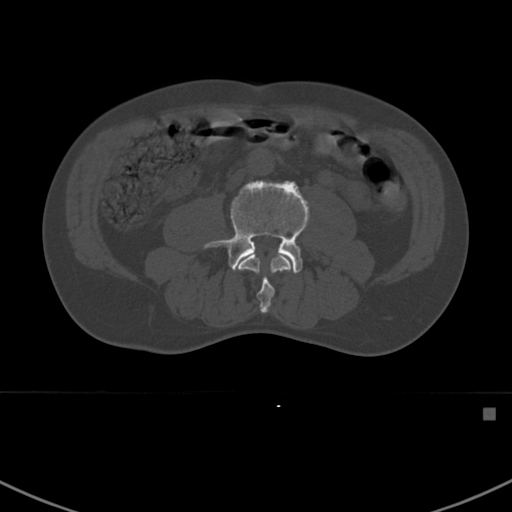
CT including the spine, one axial slice. 120 kVp. Bone window (W 1800 / L 400 HU). 1.5 mm slice thickness. 512 × 512 image matrix, field of view 358 × 358 mm. Patient: male, 59 years. From the clinical record (not read from this slice): primary cancer: prostate.
Structures marked on this image (semi-automatically segmented with operator editing):
- L3 vertebra: box from (x=236, y=253) to (x=293, y=313) px
- L4 vertebra: (x=204, y=180)–(x=310, y=274)